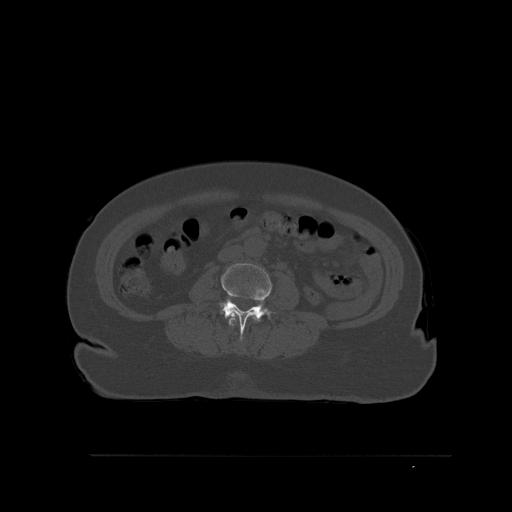
CT including the spine, one axial slice. Position 225 of 527 along the scan axis. Bone window (W 1800 / L 400 HU). 1.5 mm slice thickness. 512 × 512 image matrix. Patient: female, 73 years. Case-level facts recorded for this patient, not image findings: primary cancer: breast.
Outlined on this slice (semi-automatic segmentation, software-assisted and operator-edited):
- L2 vertebra: bounding box [x1, y1, x2, y2] px = [228, 312, 259, 327]
- L3 vertebra: [218, 263, 276, 340]